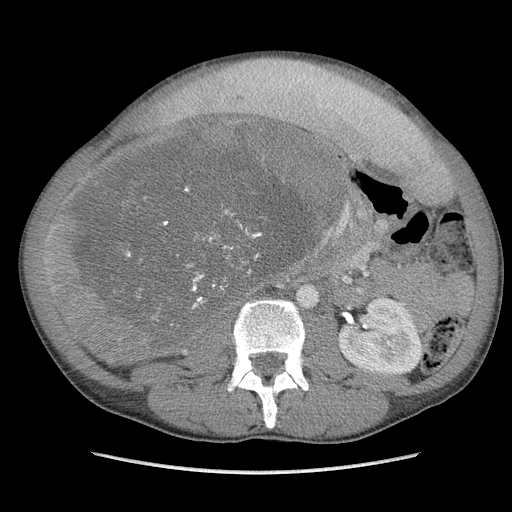
Contrast-enhanced abdominal CT, one axial slice; slice 52 of 115 in the series (ordered by position); soft-tissue window (W 400 / L 40 HU); 5 mm slice thickness; 512 × 512 image matrix, field of view 360 × 360 mm. Male patient. From the clinical record (not read from this slice): diagnosis: adrenocortical carcinoma; tumour side: right adrenal.
Outlined on this slice (semi-automatic segmentation, software-assisted and operator-edited):
- mass: bounding box <58,120,338,367> (left, top, right, bottom; pixels)